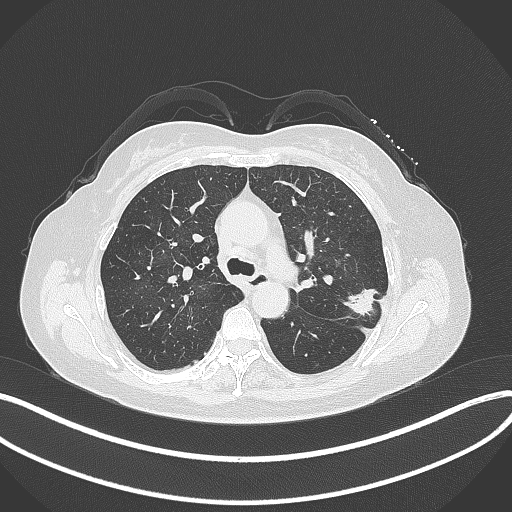
Chest CT, one axial slice. Slice 216 of 319 in the series (ordered by position). 120 kVp. Lung window (W 1500 / L -600 HU). 512 × 512 image matrix, field of view 400 × 400 mm. Female patient, age 60 years. Case-level facts recorded for this patient, not image findings: clinical TNM (as recorded): T1c N0 M0.
Outlined on this slice (bounding box drawn by a radiologist):
- lung tumour (recorded histology: adenocarcinoma): bounding box [x1, y1, x2, y2] px = [345, 283, 380, 319]